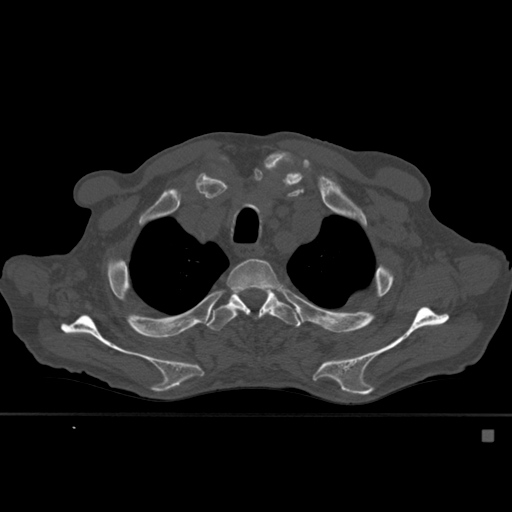
CT including the spine, one axial slice; slice 424 of 527 in the series (ordered by position); bone window (W 1800 / L 400 HU); 512 × 512 image matrix, field of view 373 × 373 mm. Patient: male, 78 years. From the clinical record (not read from this slice): primary cancer: prostate.
Outlined on this slice (semi-automatic segmentation, software-assisted and operator-edited):
- T3 vertebra: bounding box <226,259,282,316> (left, top, right, bottom; pixels)
- T4 vertebra: <206,286,301,331>